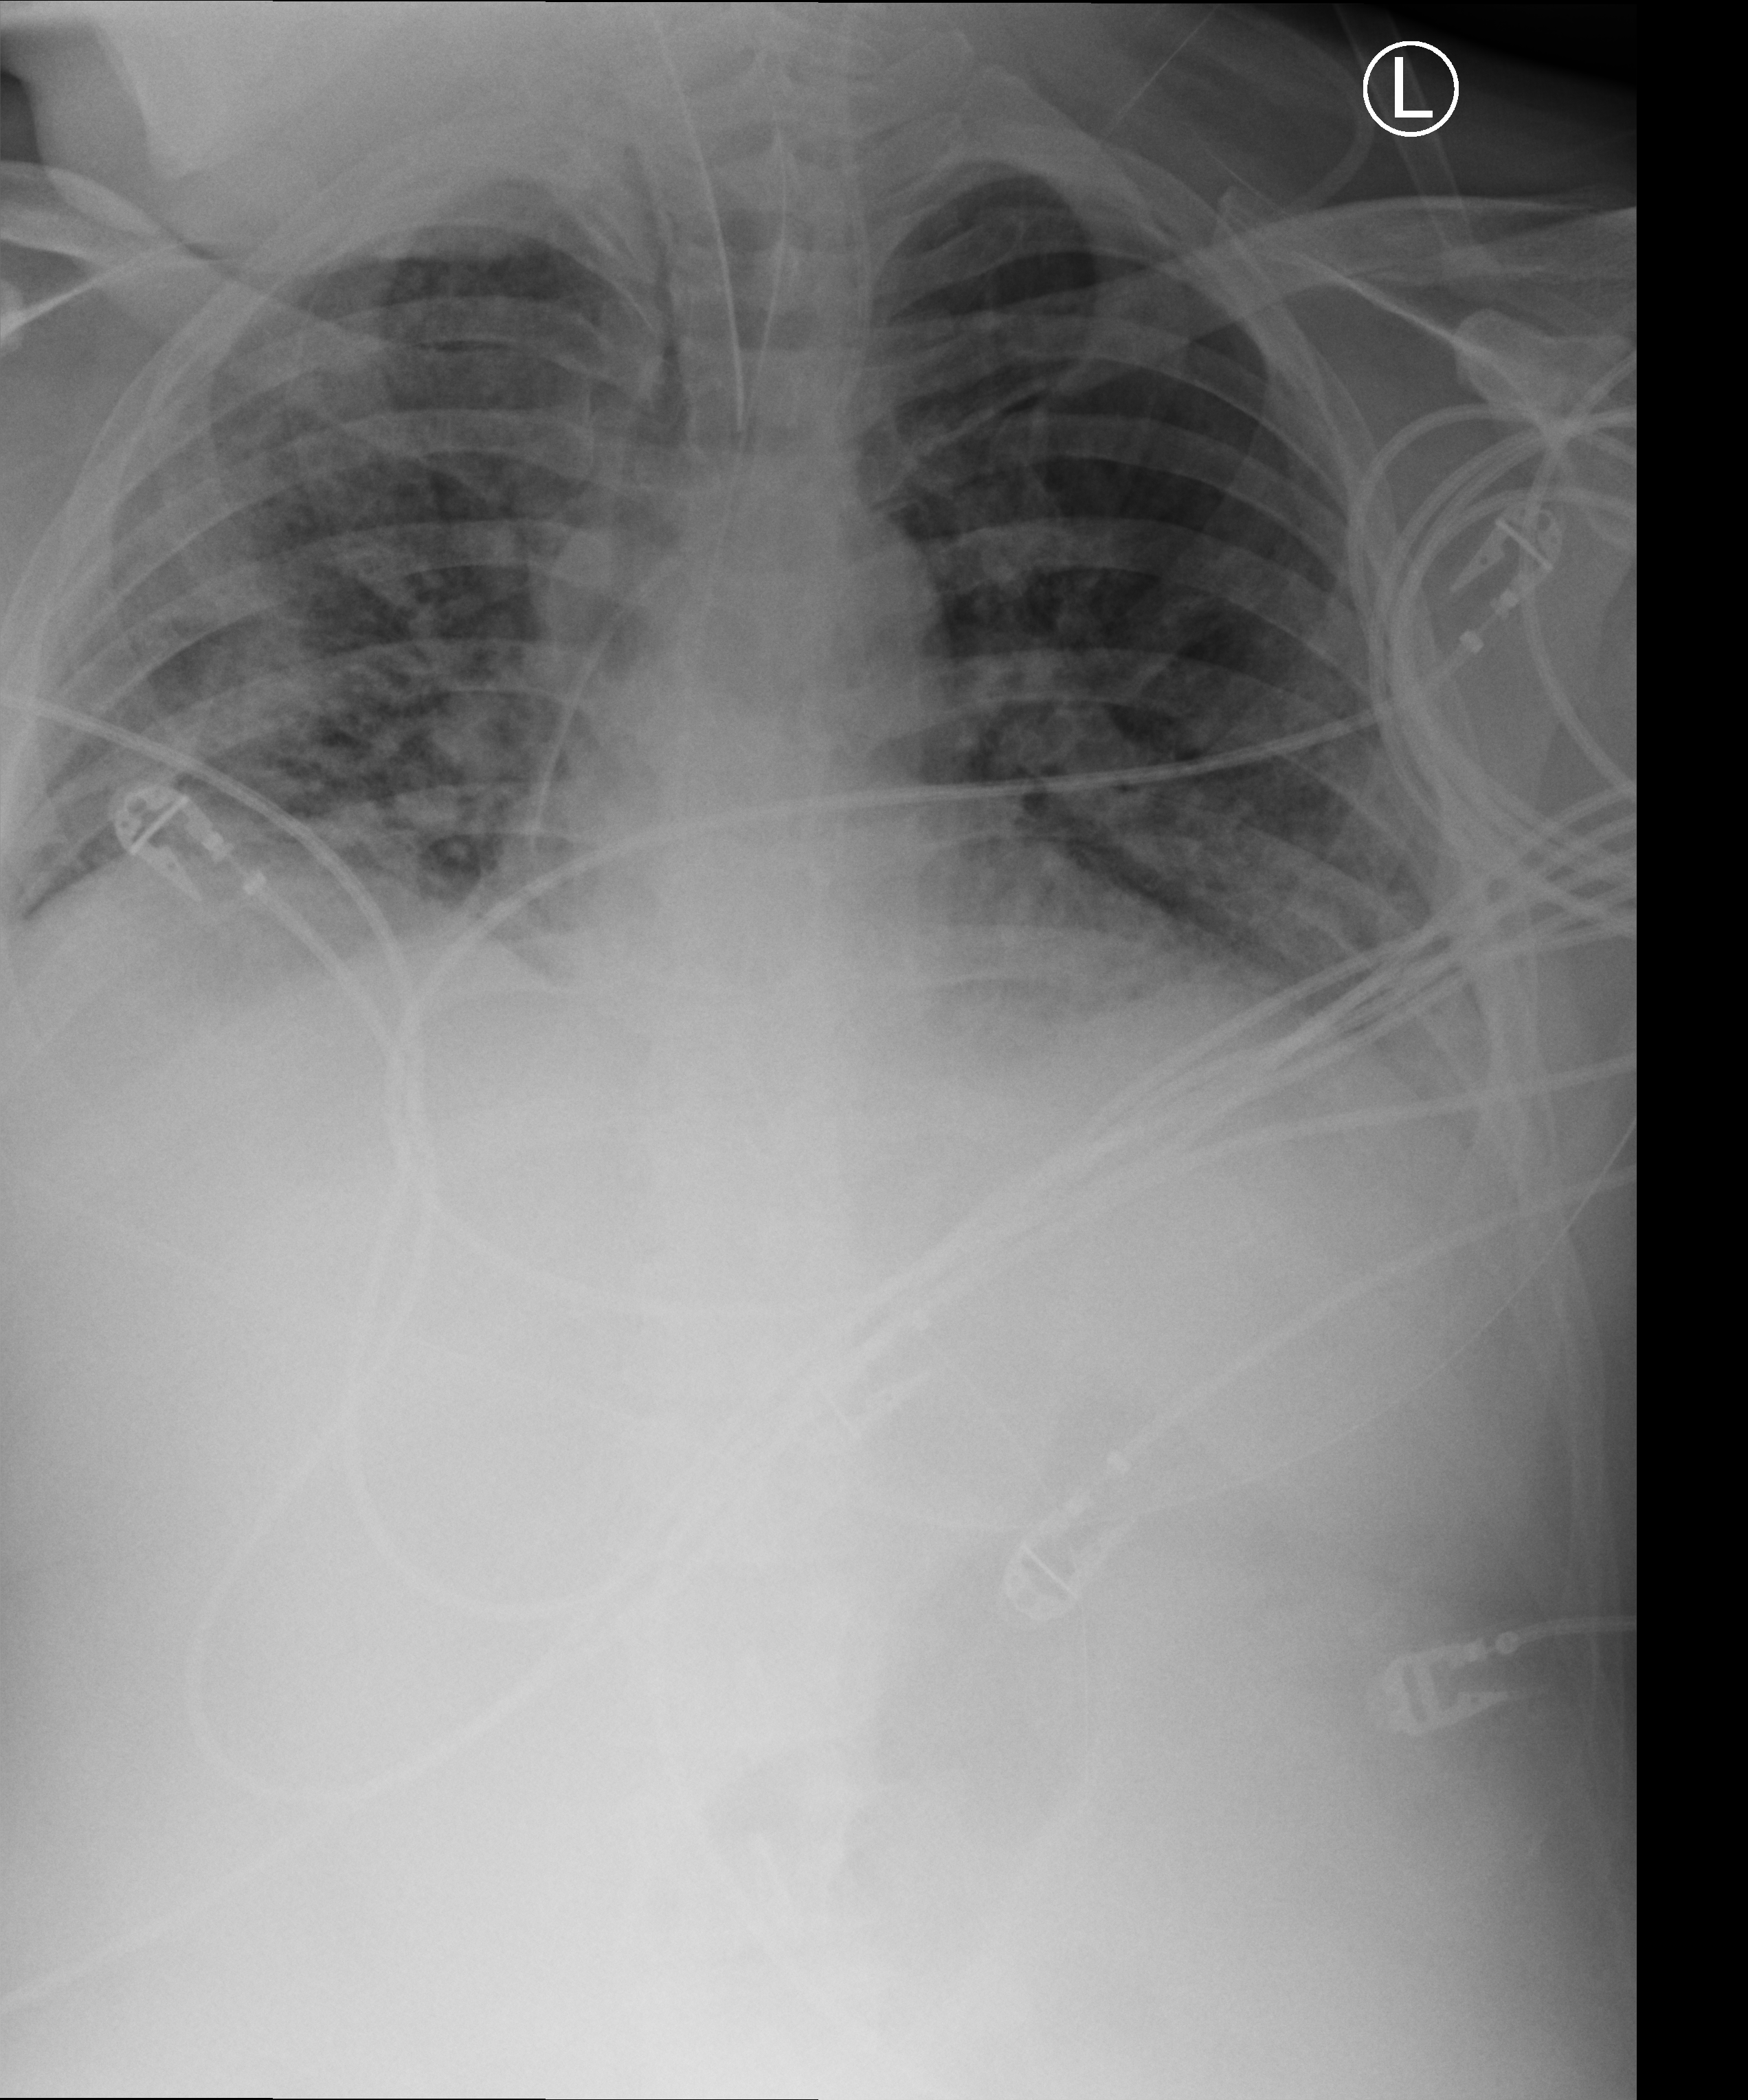
Chest X-ray (portable); anteroposterior (AP) projection. Patient hospitalised with COVID-19; male, aged 18–59 years.
Admission-level facts for this patient (not findings on this image; timing relative to this image not recorded): mechanically ventilated during this hospital stay: yes.